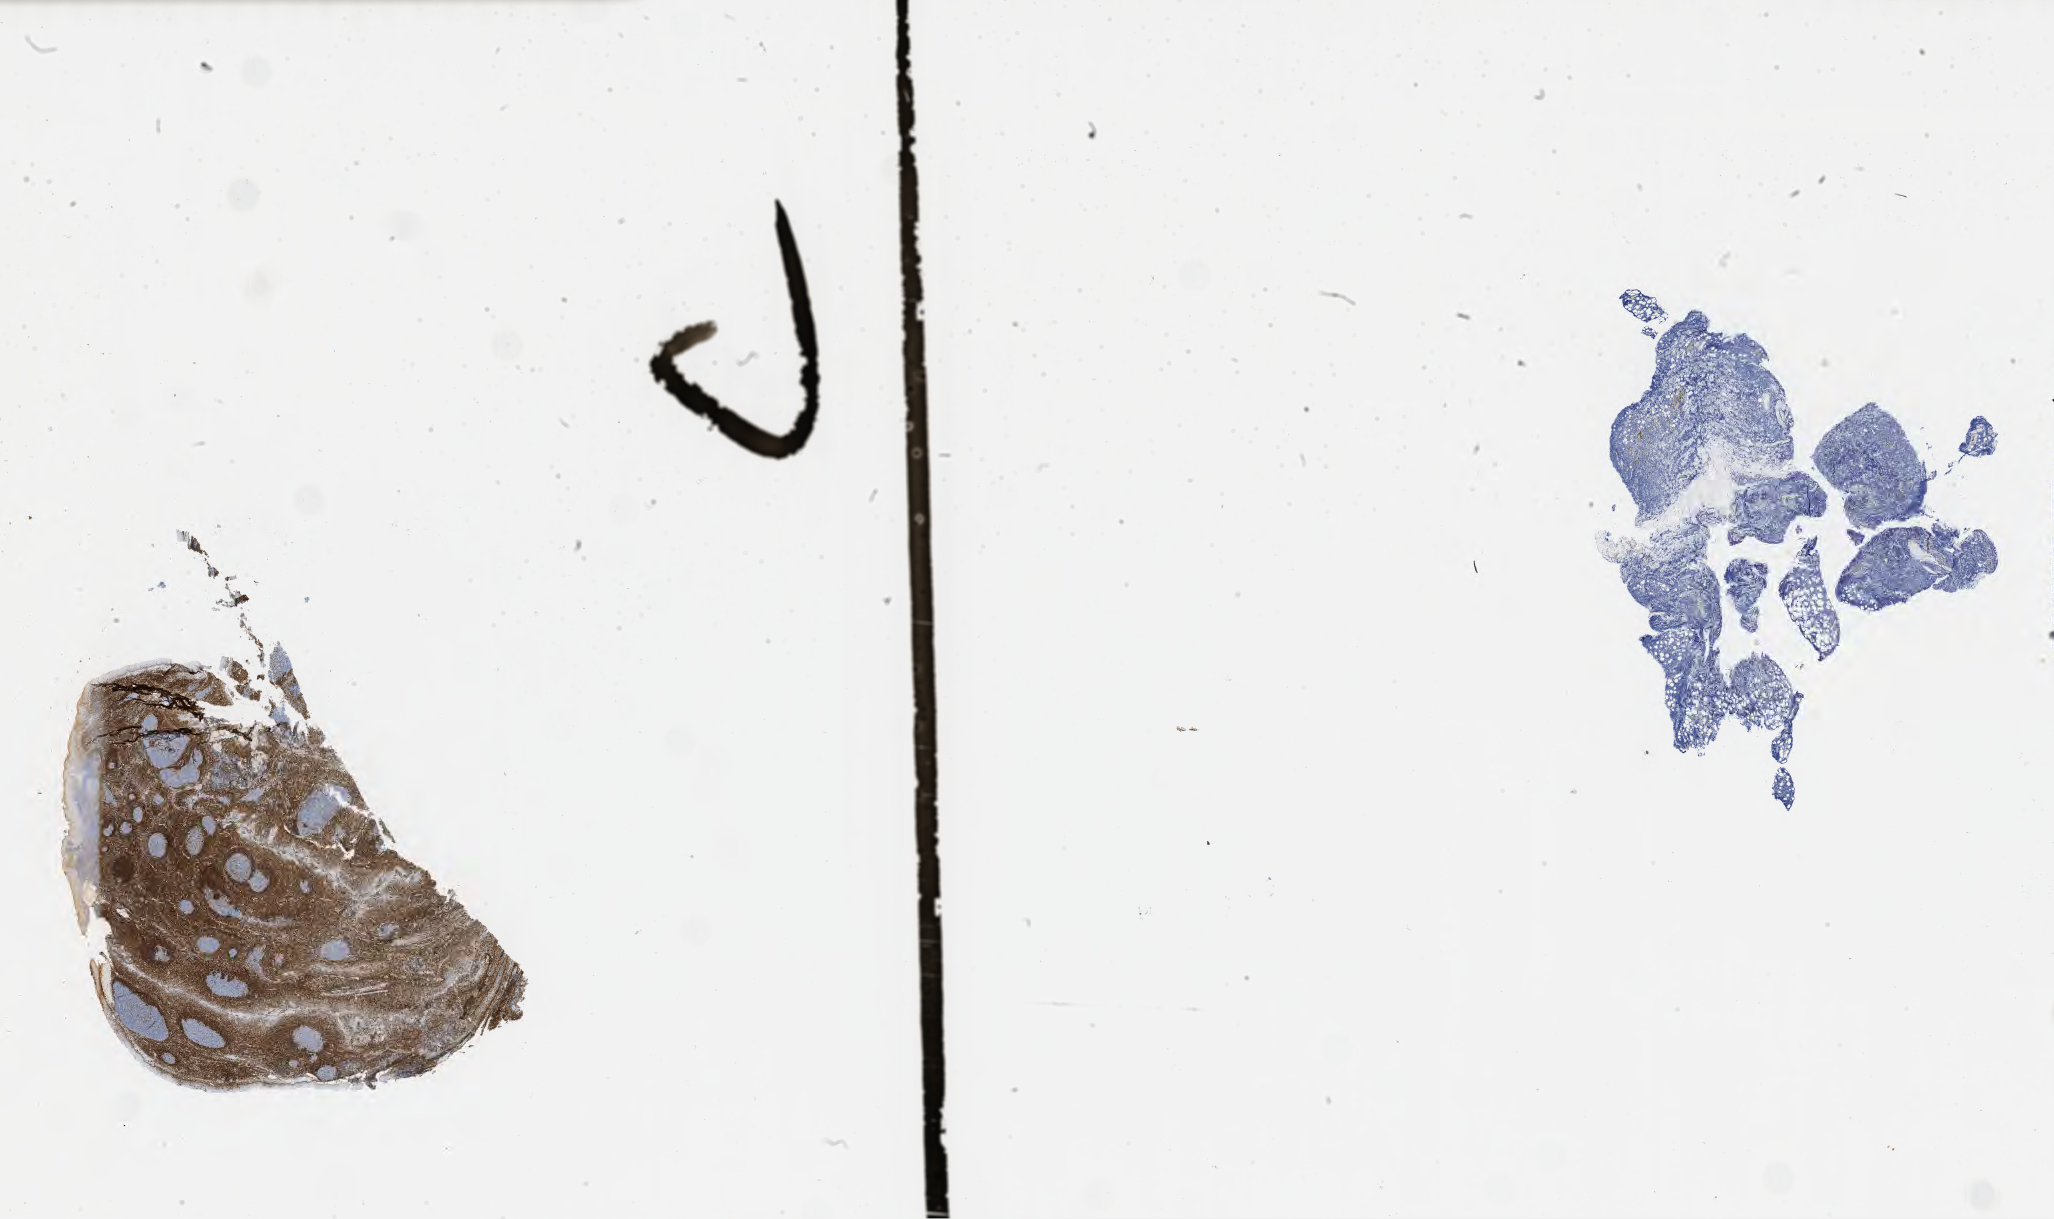
Whole-slide image, immunohistochemical stain for BCL2, a low-resolution overview of the entire scanned area, about 33.2 x 19.7 mm, tumor tissue, anatomic site: orbit. Patient male; 20 years old.
Histologic diagnosis: Burkitt lymphoma, NOS.